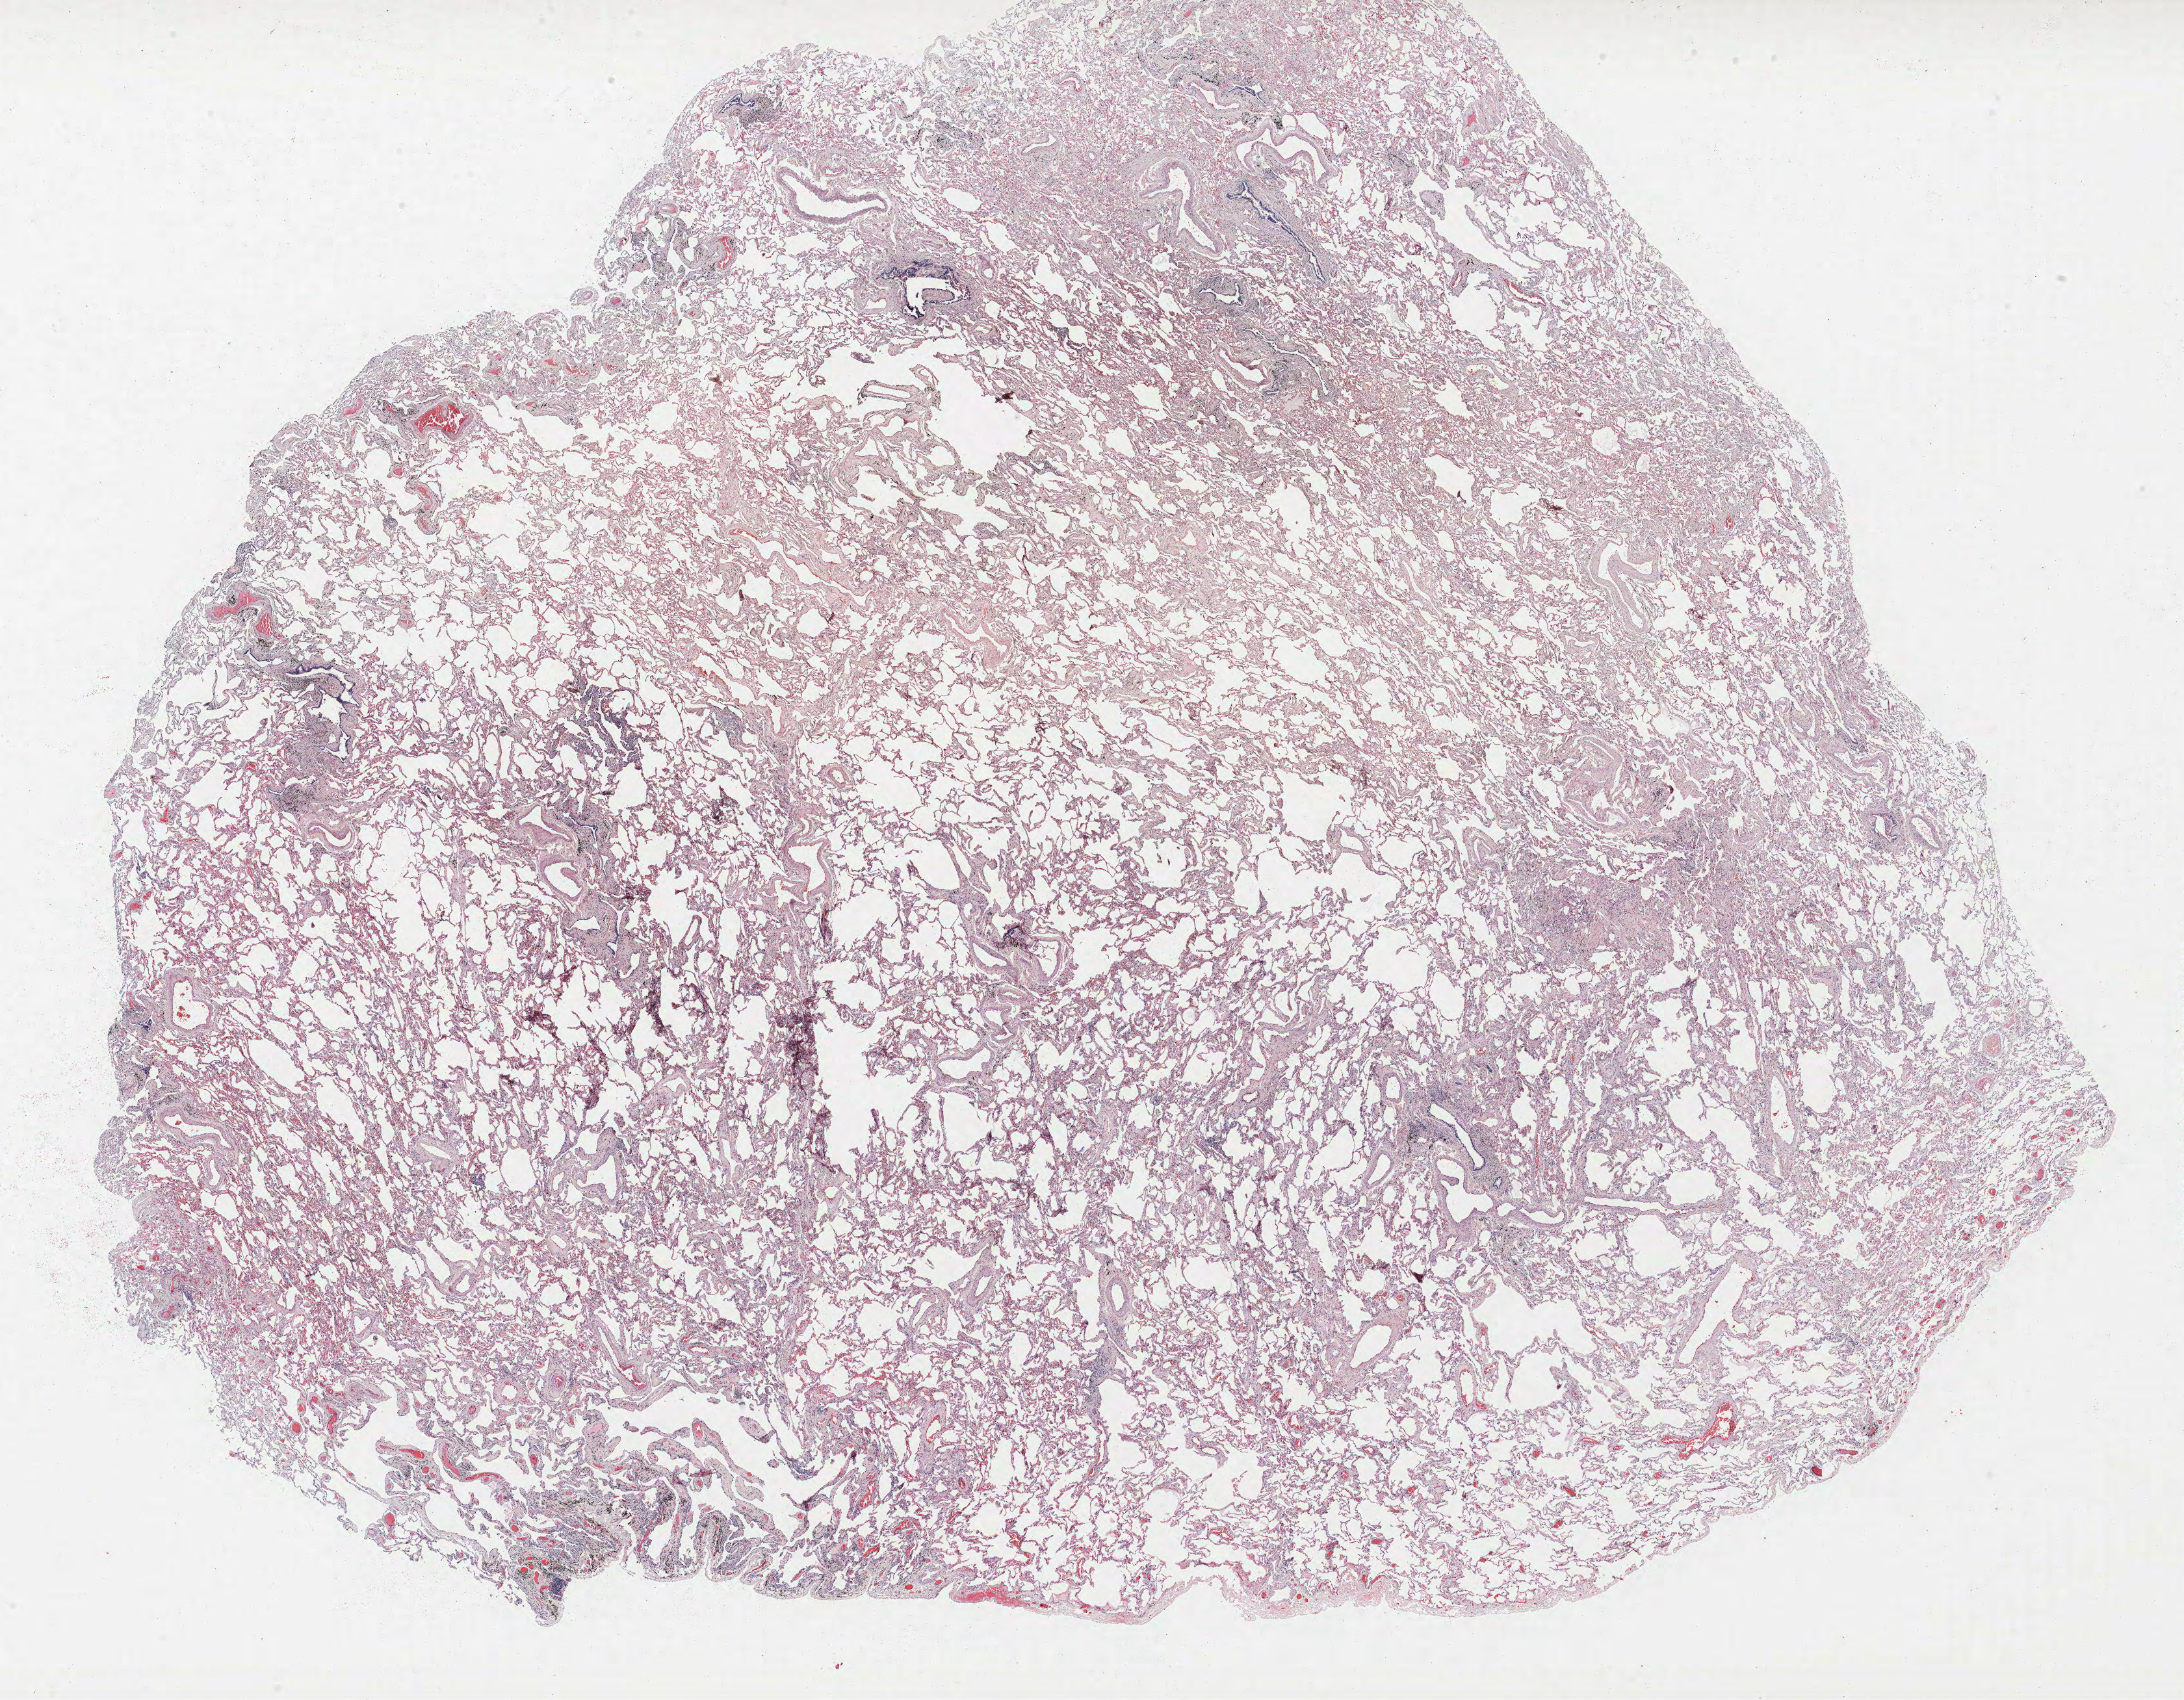
Whole-slide histology image, H&E — shown as a low-resolution overview of the whole scanned area (about 26.9 x 20.9 mm, slide scanned at 40x). FFPE section. Lung. Male, age 67 at enrolment. Former smoker at enrolment. Grade: moderately differentiated (G2).
Participant's lung-cancer diagnosis: Squamous cell carcinoma, large cell, nonkeratinizing, NOS. ICD-O-3 topography: upper lobe of lung (C34.1). Stage (AJCC 6th edition): IA. Primary tumour location (clinical record): left upper lobe. Tumour size (pathology): 15 mm.